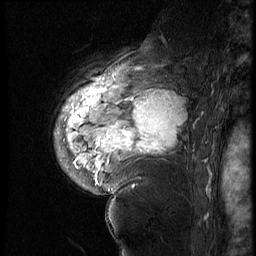
Breast MRI (dynamic contrast-enhanced), one sagittal slice; slice 46 of 60 in the series (ordered by position); 4 images stored at this slice position (order not interpretable as contrast timing); 1.5 T; TE 4.2 ms, TR 9 ms; 256 × 256 image matrix. Patient: female, 56 years. Case-level facts recorded for this patient, not image findings: setting: breast cancer imaged before/during neoadjuvant chemotherapy; receptor status: HER2-positive.
Annotated regions visible in this slice (semi-automatically segmented with operator editing):
- analysis volume of interest (the breast-tissue region the enhancement analysis was run in; not a lesion): bounding box (x1, y1, x2, y2) in pixels: (82, 83, 199, 177)
- tumour enhancement mask (voxels above the 140 % enhancement threshold inside the analysis volume of interest): (105, 93, 185, 154)